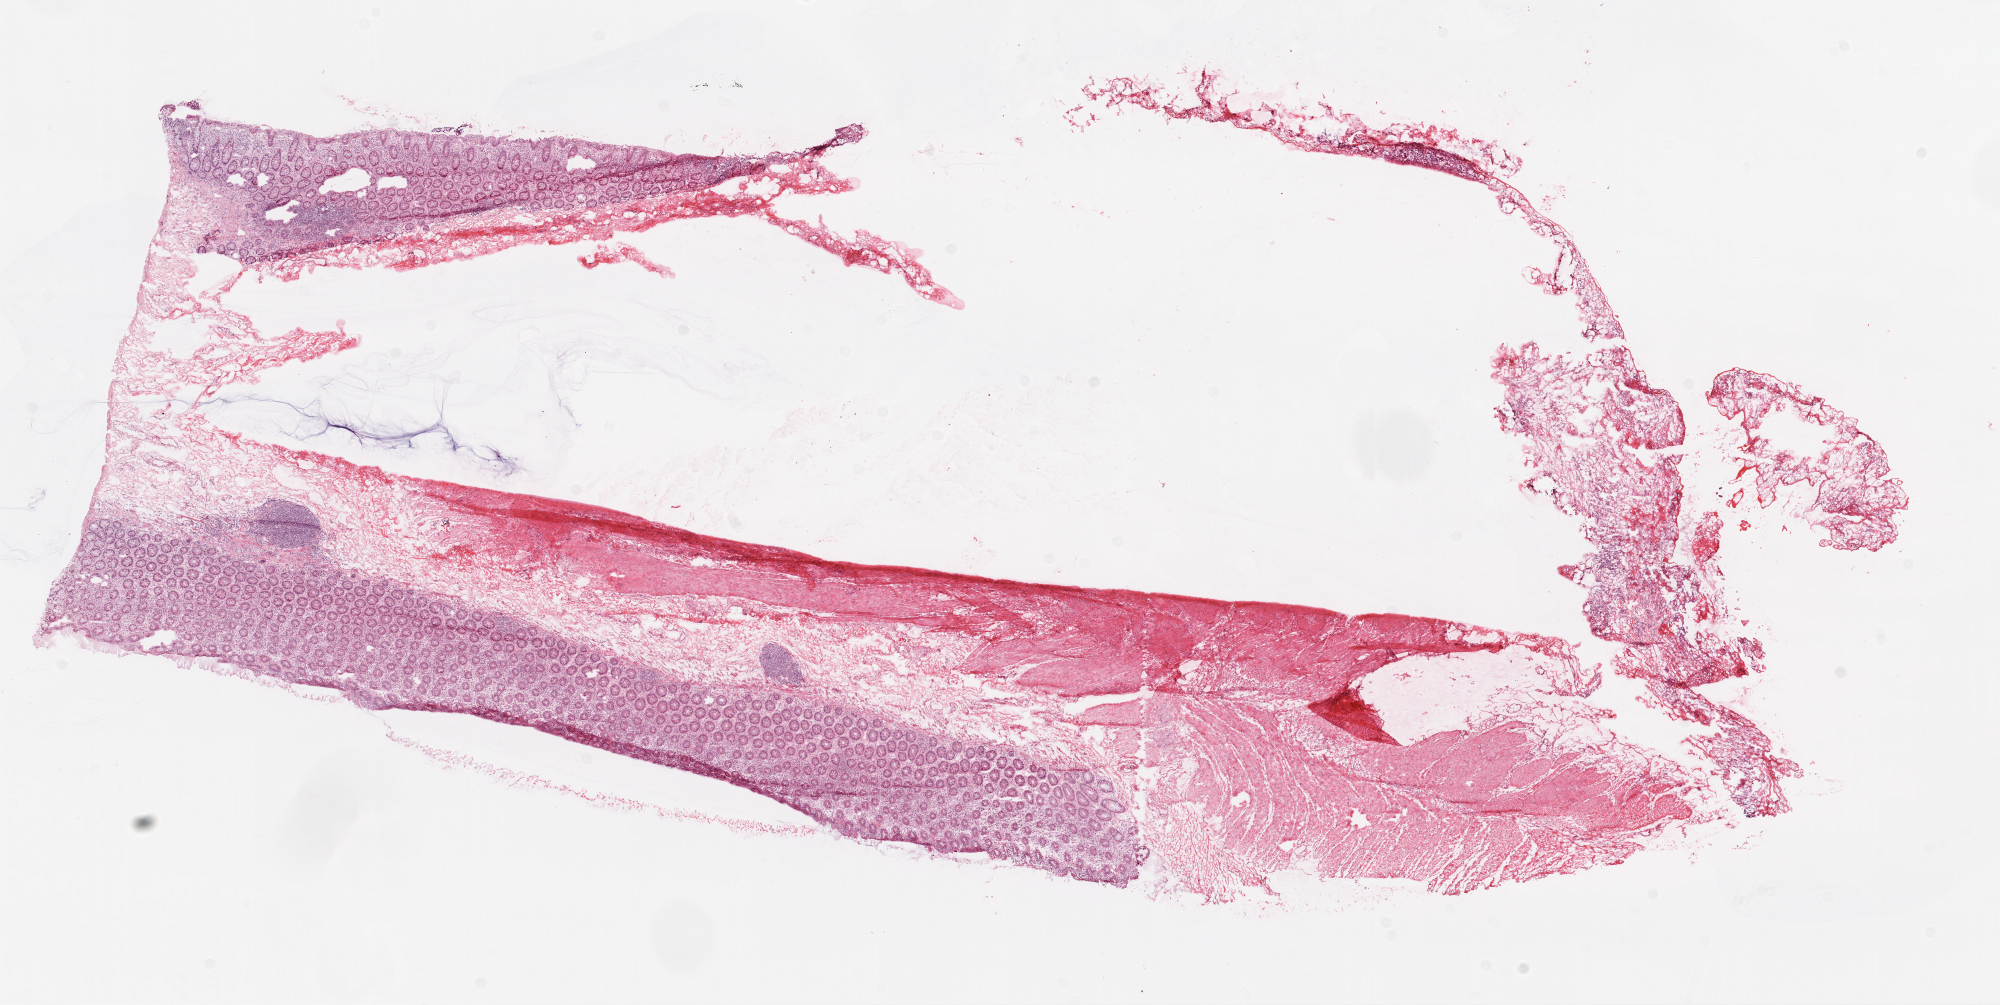
Digitized H&E-stained tissue section (whole slide), whole scanned area (about 16.0 x 8.1 mm, from a 20x scan) shown as a low-resolution overview. Frozen section from the top of the tissue portion. Ovary, solid tissue normal (non-tumour tissue) sample. Patient: female, age at initial diagnosis 63 years.
This section: solid tissue normal (non-tumour) sample from the same patient. Patient diagnosis: Serous cystadenocarcinoma, NOS.